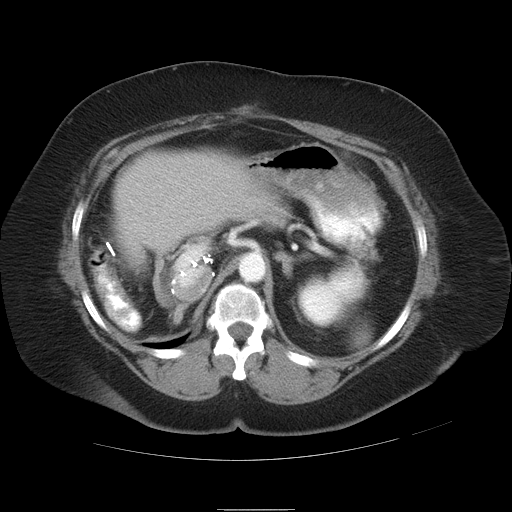
Contrast-enhanced abdominal CT, one axial slice; slice 22 of 37 in the series (ordered by position); reconstruction kernel STANDARD; intravenous contrast given; soft-tissue window (W 400 / L 40 HU); 7.5 mm slice thickness; 512 × 512 image matrix, field of view 422 × 422 mm. Female patient, age 68 years. From the clinical record (not read from this slice): diagnosis: colorectal cancer liver metastases, imaged before liver resection; multiple liver metastases: no; largest metastasis: 2 cm; chemotherapy before resection: no.
Annotated regions visible in this slice (manually delineated by an expert):
- liver: bounding box [x1, y1, x2, y2] px = [114, 151, 278, 268]
- planned liver remnant (the part of the liver to remain after resection): [115, 151, 278, 252]
- portal vein (with intrahepatic branches): [175, 245, 209, 288]